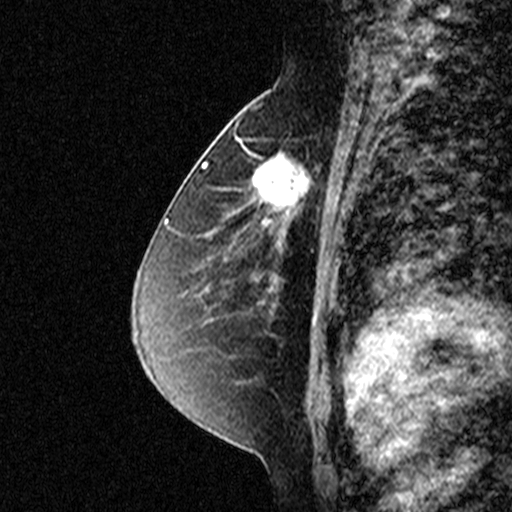
Breast MRI (dynamic contrast-enhanced), one sagittal slice; dynamic contrast-enhanced study with each time point stored as its own series, time point 2 of 3 at this slice position (early post-contrast, ordered by acquisition time); 1.5 T; TE 4.5 ms, TR 11 ms; 512 × 512 image matrix, field of view 200 × 200 mm. Patient: female, 49 years. Case-level facts recorded for this patient, not image findings: setting: breast cancer imaged before/during neoadjuvant chemotherapy; receptor status: triple-negative.
Outlined on this slice (semi-automatically segmented with operator editing):
- analysis volume of interest (the breast-tissue region the enhancement analysis was run in; not a lesion): bounding box (x1, y1, x2, y2) in pixels: (238, 122, 331, 227)
- tumour enhancement mask (voxels above the 90 % enhancement threshold inside the analysis volume of interest): (238, 138, 316, 222)